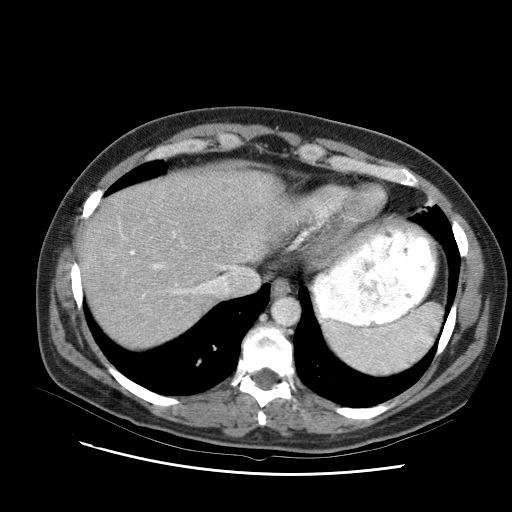
Contrast-enhanced abdominal CT (liver protocol), one axial slice; slice 80 of 95 in the series (ordered by position); 120 kVp; one of 2 acquisitions stored at this slice position; soft-tissue window (W 400 / L 40 HU); 2.5 mm slice thickness; 512 × 512 image matrix, field of view 360 × 360 mm. From the clinical record (not read from this slice): diagnosis: hepatocellular carcinoma (patient treated with transarterial chemoembolisation; whether this scan precedes or follows treatment is not stated here); TNM stage (as recorded): Stage-I; Child-Pugh class: B; tumour differentiation: moderately differentiated.
Annotated regions visible in this slice (semi-automatically segmented with operator editing):
- liver parenchyma outside the tumour (the mass and vessels are separate outlines, so this box may not span the whole liver): box from (x=82, y=178) to (x=248, y=322) px
- liver vessels: (x=121, y=222)–(x=177, y=269)